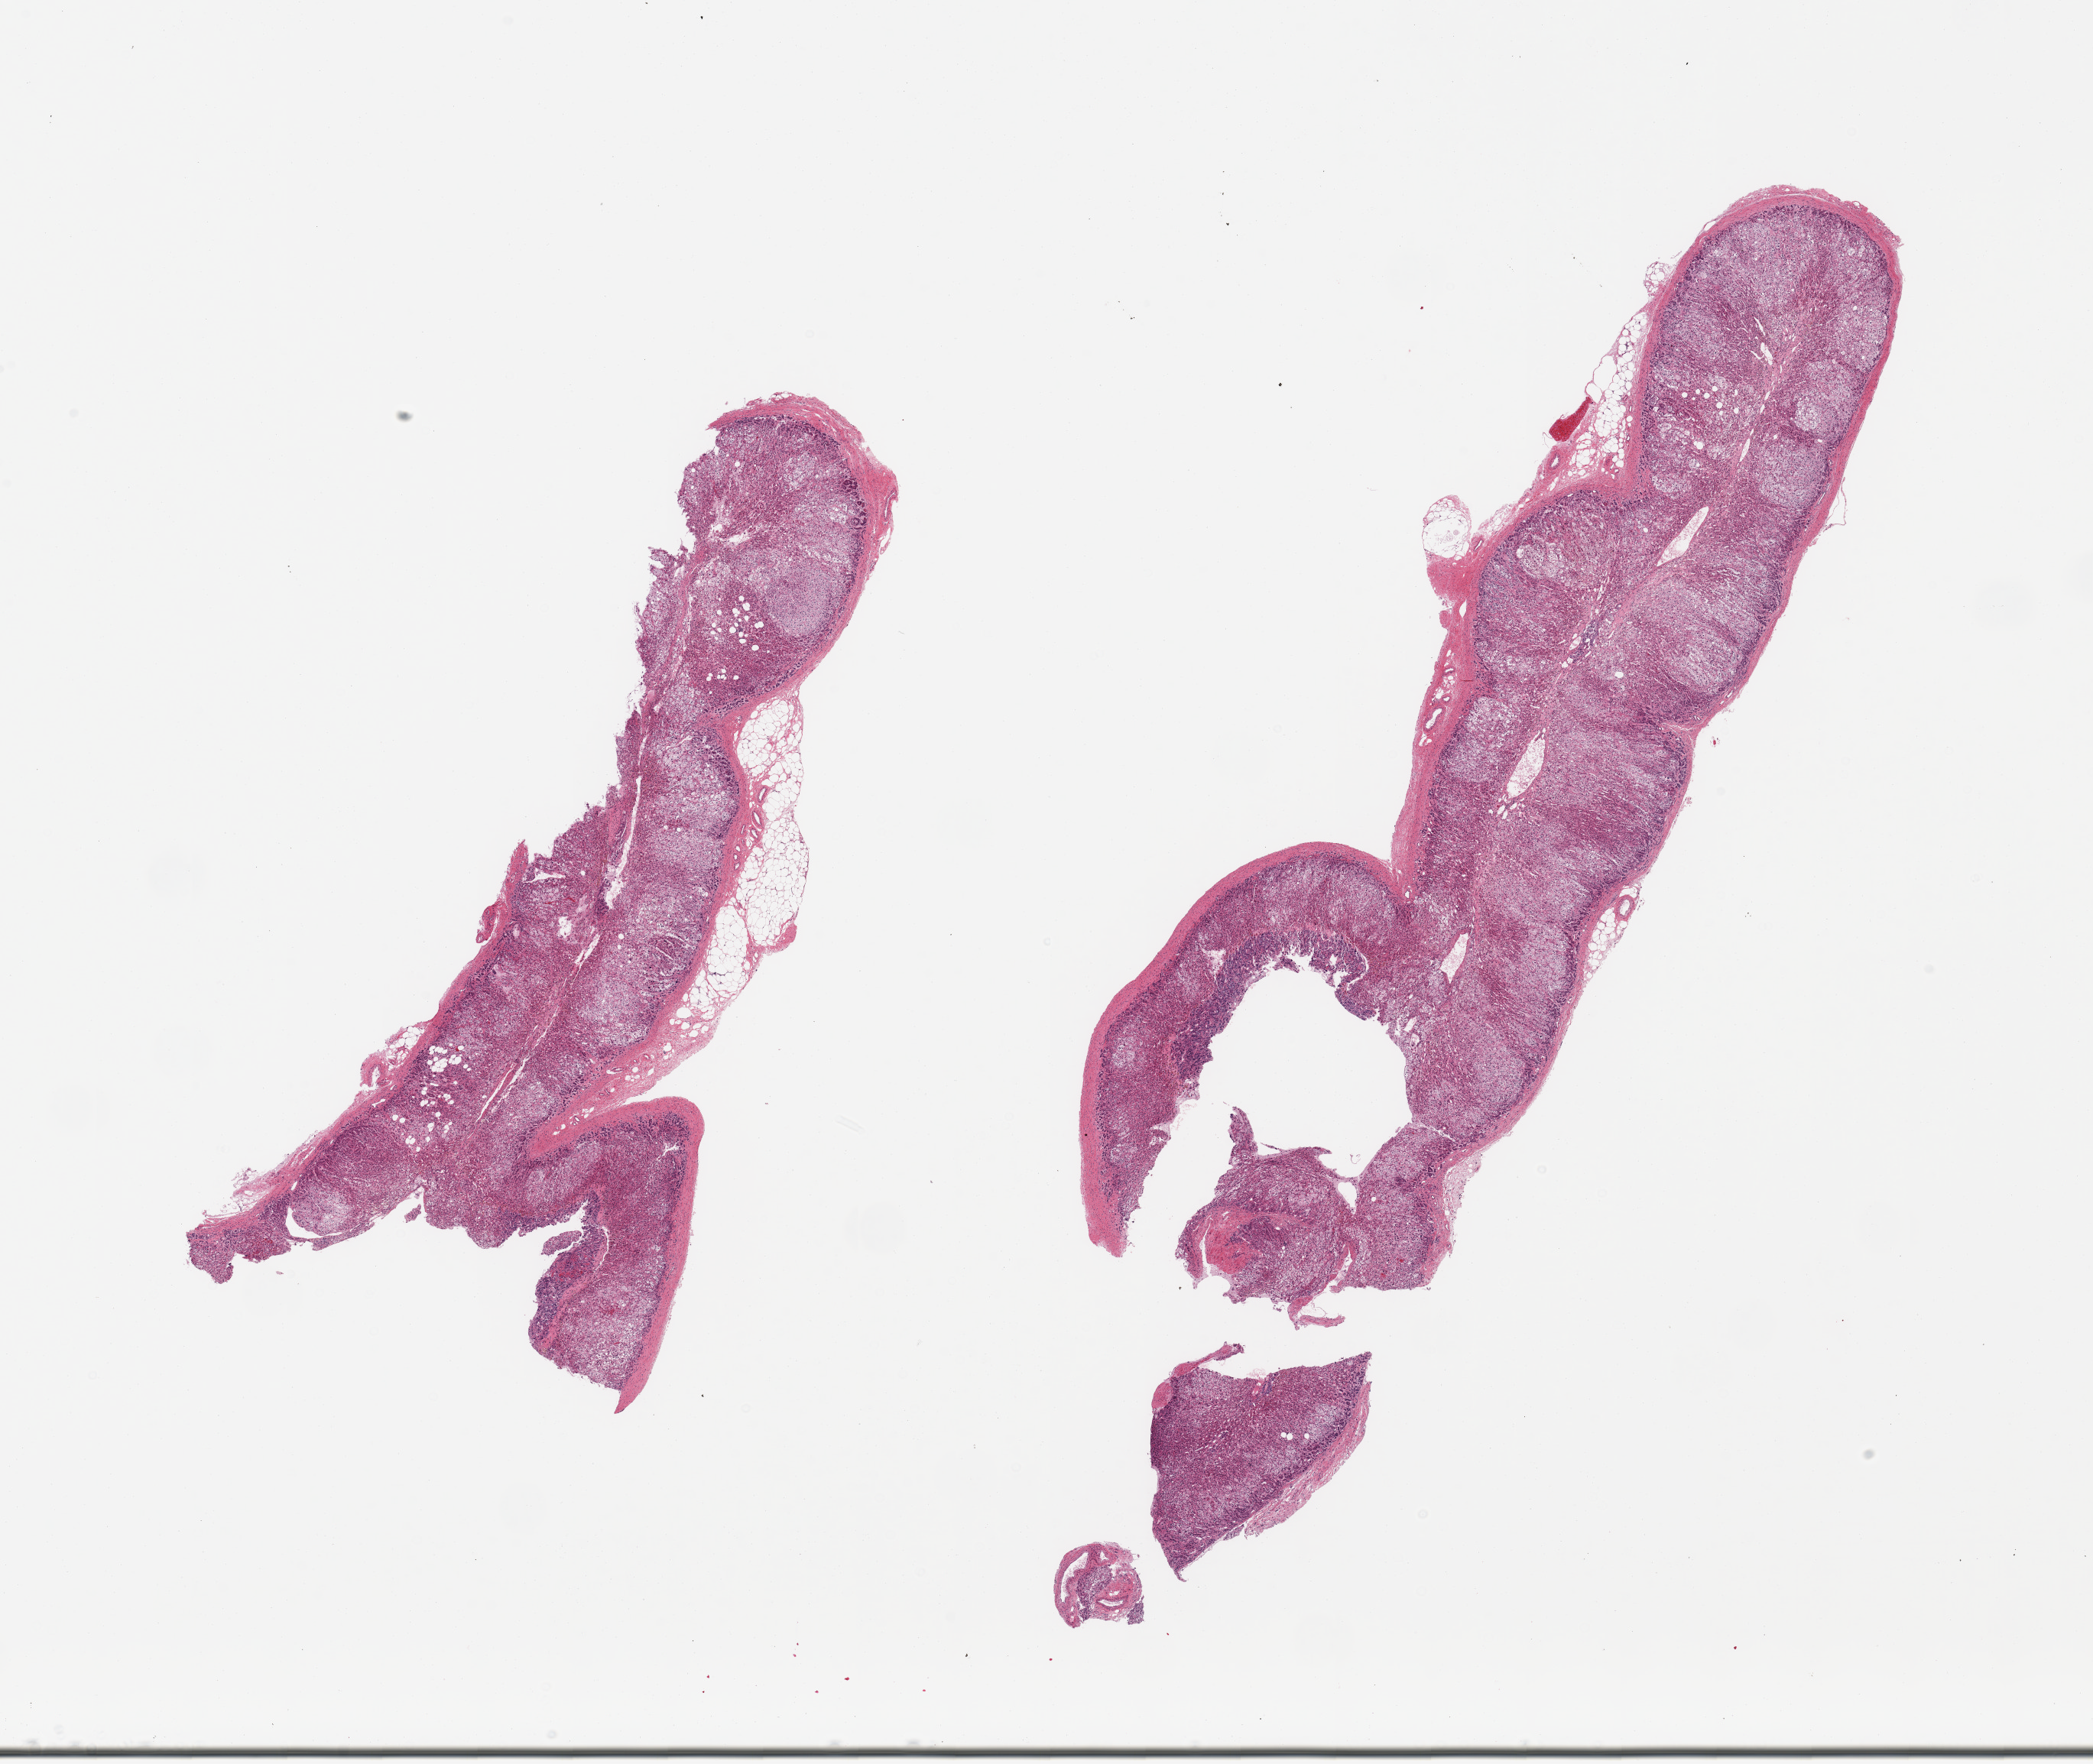
Digitized H&E-stained section, brightfield — shown as a low-resolution overview of the whole scanned area (about 21.7 x 18.3 mm), PAXgene-fixed, paraffin-embedded tissue, sampled site (target tissue): adrenal gland, tissue donor sample. Donor: male.
* reviewer comment on this tissue sample: 2 pieces; attached fat, up to ~10% on 1 piece, cortex and medulla